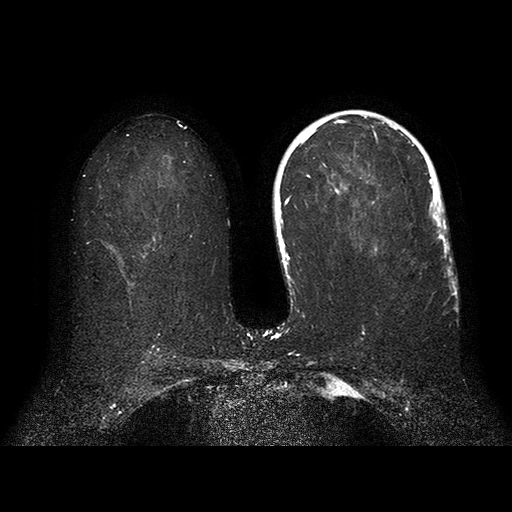
MRI of the breasts; 2 images, each one mid-volume slice chosen by position. Age decade 40s.
Image 1: axial T2-weighted / STIR image, series "T2 STIR AX SENSE", slice 53 of 105.
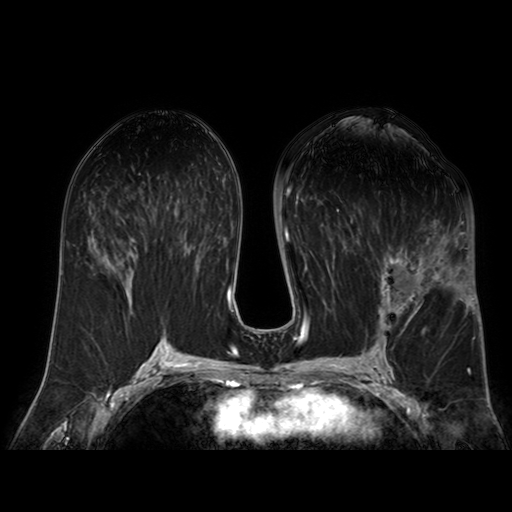
Image 2: axial dynamic contrast-enhanced T1-weighted image, series "AX BLISS_AUTO SENSE", slice 50 of 98, dynamic phase 5 of 8, 4 mm slice thickness.
Patient-level pathology facts (from the clinical record, not from the images): pathology diagnosis: invasive ductal CA (left breast); receptor status (as recorded): ER pos, PR pos, HER2 pos.